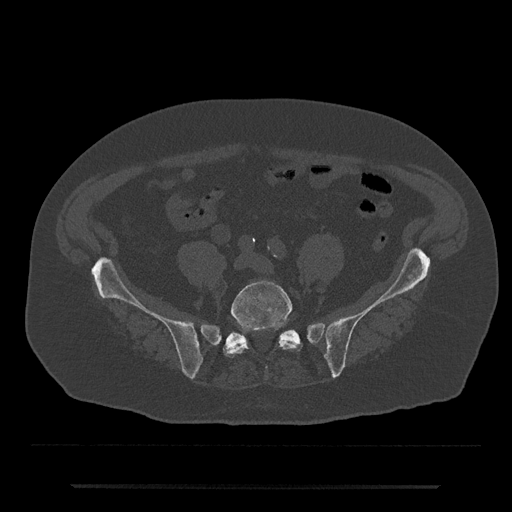
CT including the spine, one axial slice; position 269 of 797 along the scan axis; reconstruction kernel Br40s/3; bone window (W 1800 / L 400 HU); 0.5 mm slice thickness; 512 × 512 image matrix. Male patient, age 80 years. Case-level facts recorded for this patient, not image findings: primary cancer: prostate; vertebrae with lytic lesions (as recorded): L1, T11.
Structures marked on this image (semi-automatic segmentation, software-assisted and operator-edited):
- L5 vertebra: bounding box [x1, y1, x2, y2] px = [223, 280, 299, 357]